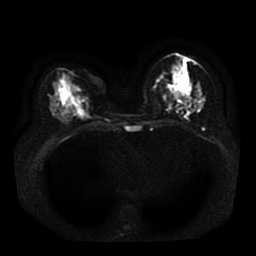
Breast MRI, one axial slice; position 14 of 41 along the scan axis; diffusion-weighted series; image 2 of 4 stored at this slice position (different b-values; order by instance number); 1.5 T; 256 × 256 image matrix, field of view 330 × 330 mm. Female patient.
Annotated regions visible in this slice (expert manual segmentation):
- tumour on diffusion-weighted imaging: bounding box (x1, y1, x2, y2) in pixels: (175, 93, 178, 95)